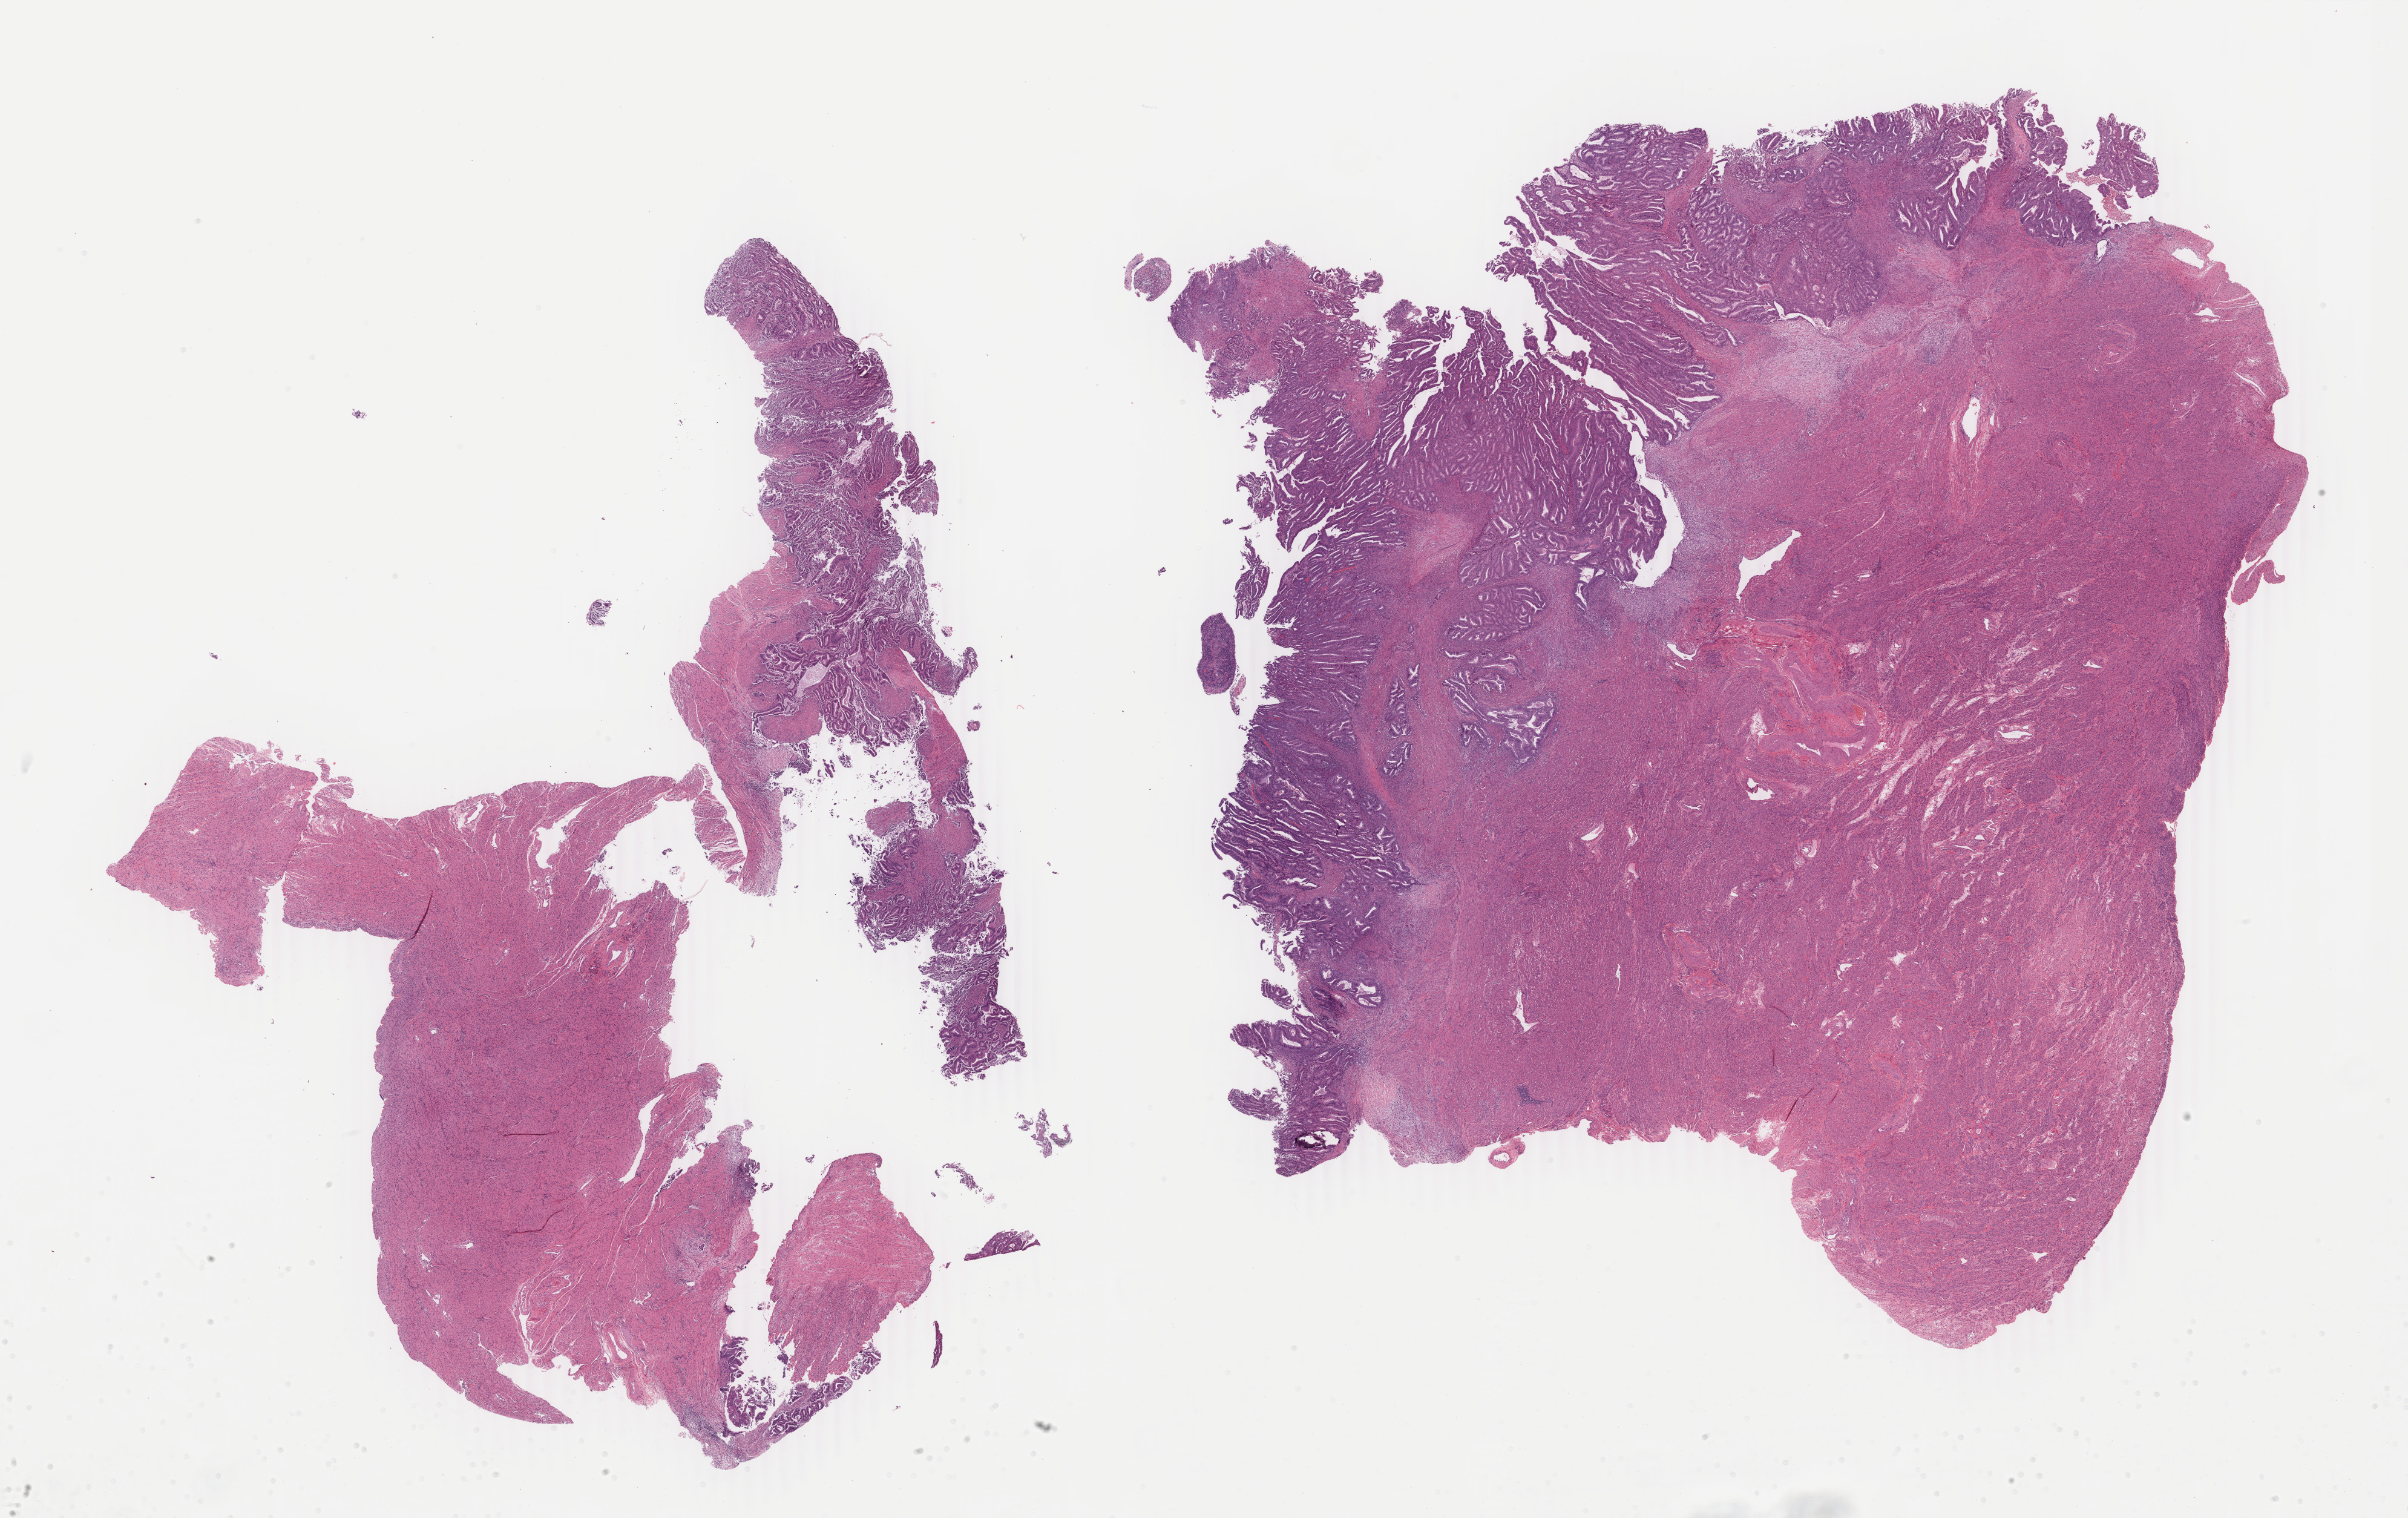
Whole-slide histology image, H&E-stained, whole scanned area (about 31.6 x 19.9 mm, acquisition: 40x scan) shown as a low-resolution overview, FFPE section, primary tumour sample from the uterus. Female, age 61 years at initial diagnosis.
Pathologic diagnosis: Endometrioid adenocarcinoma, NOS (endometrium).